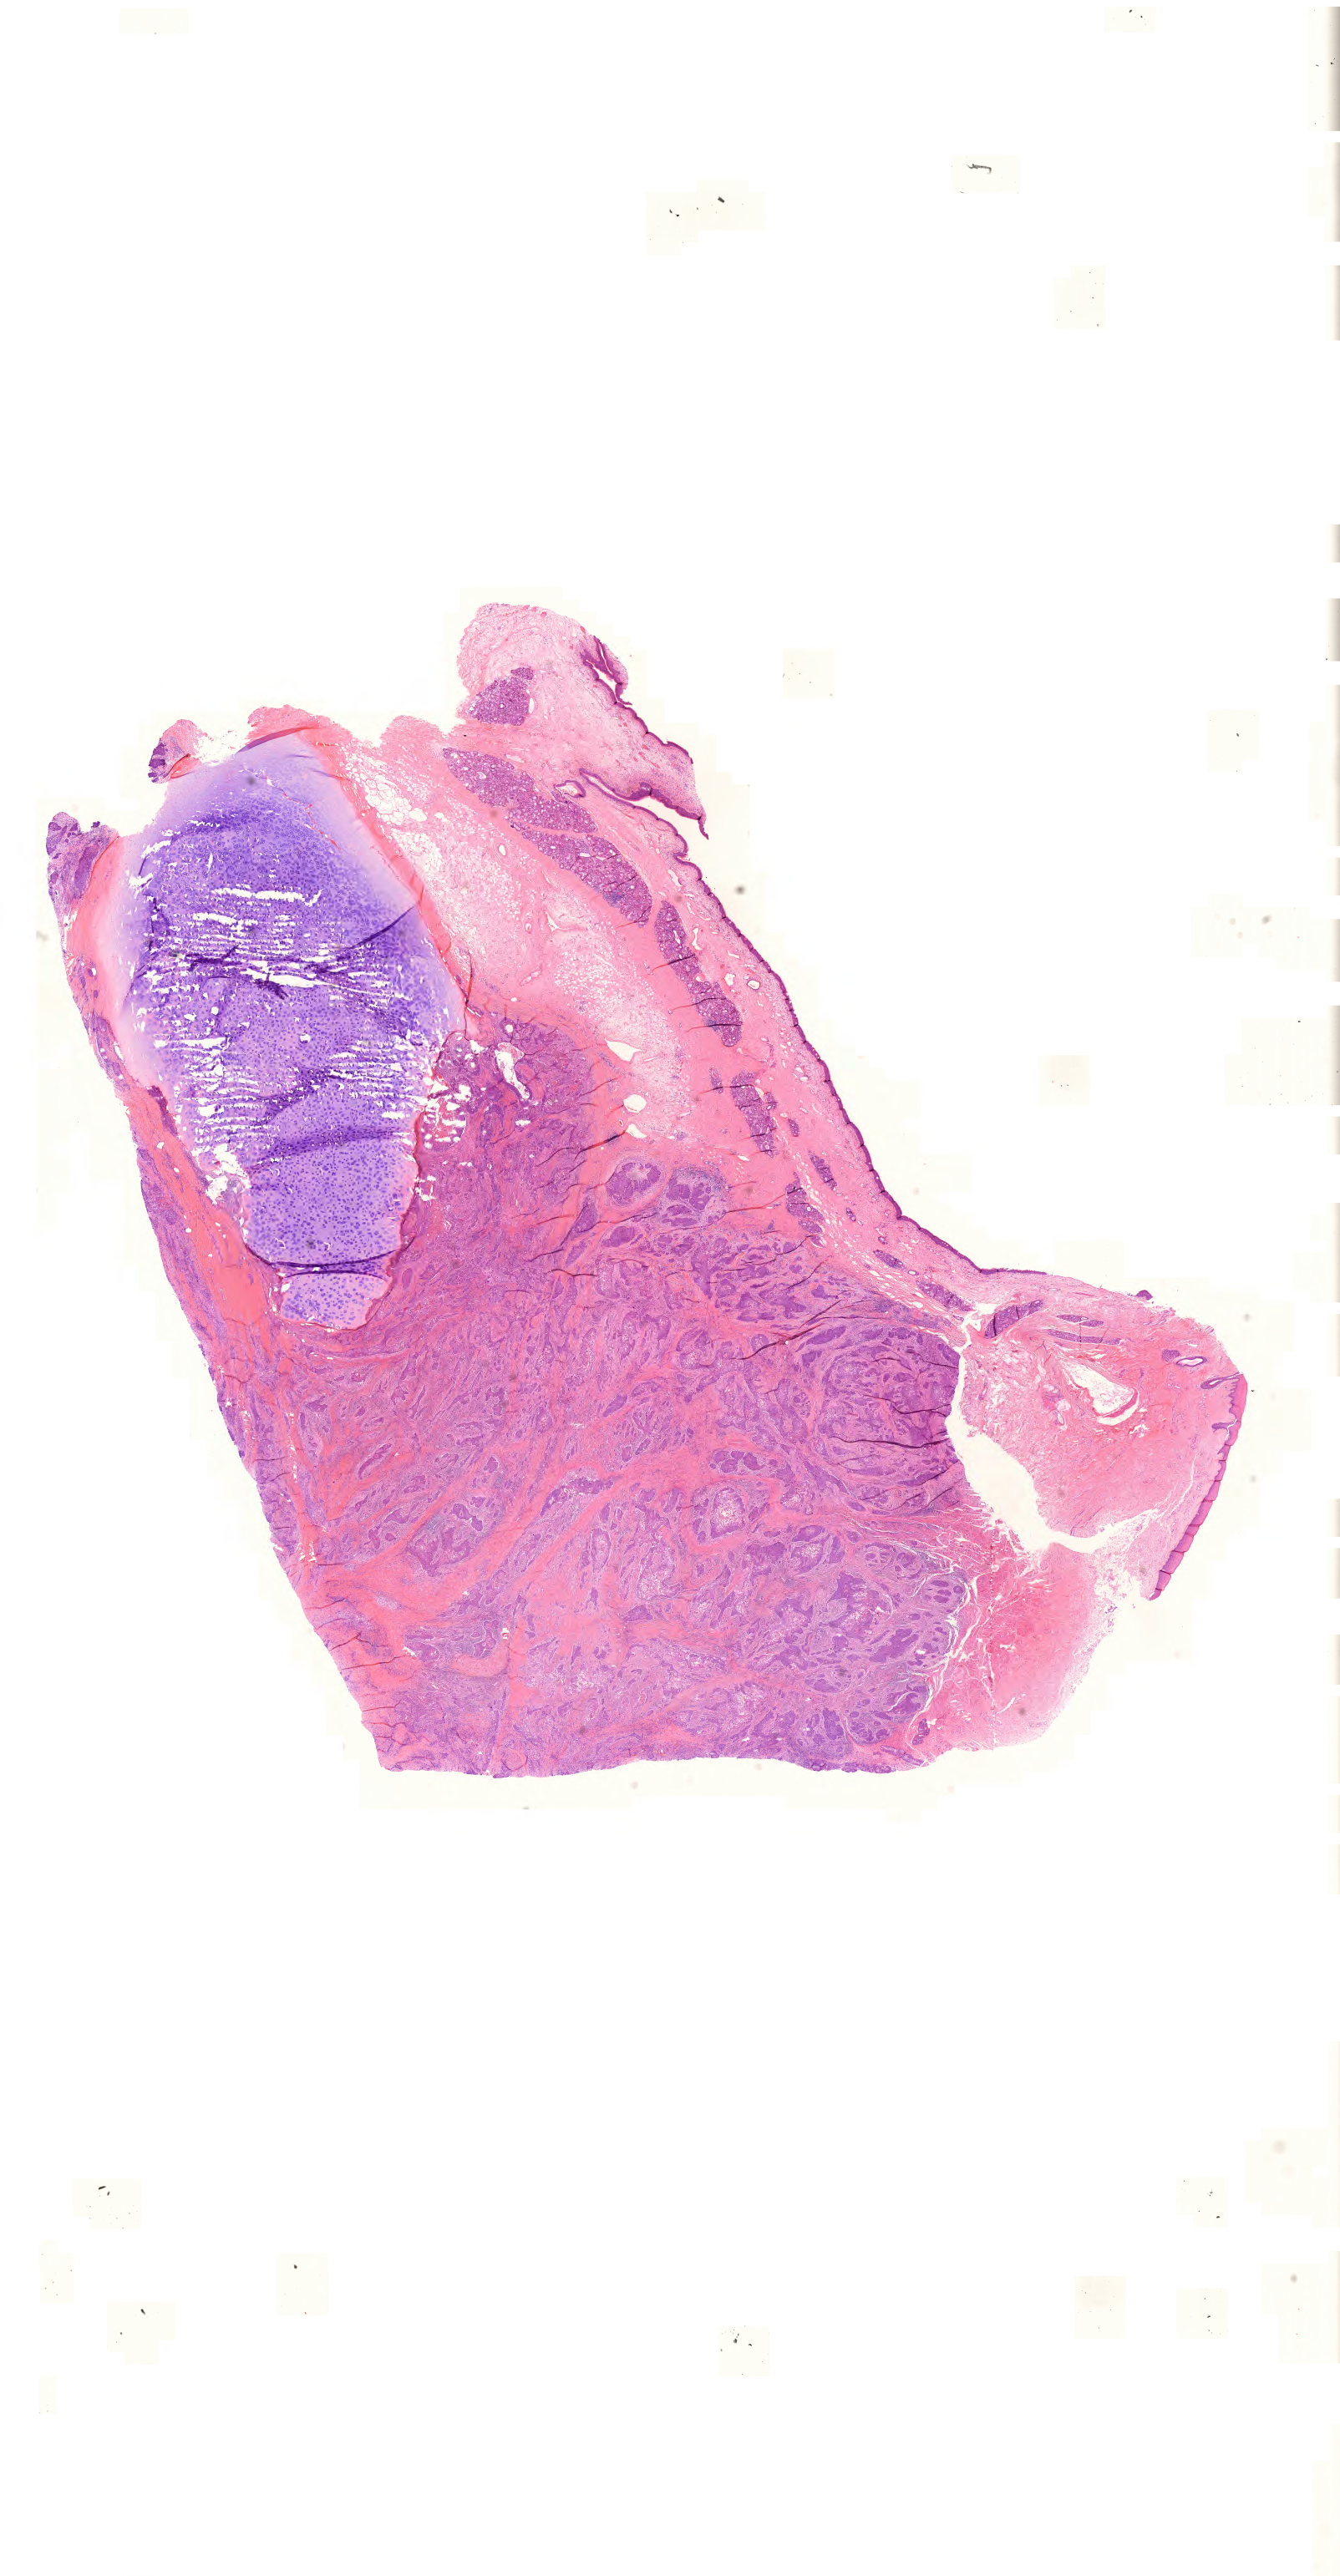
Whole-slide histology image, H&E — low-resolution overview of the scanned area, about 23.9 x 45.9 mm; formalin-fixed paraffin-embedded (FFPE) diagnostic section; sample: primary tumour, head and neck. Patient: male, age at initial diagnosis 52 years. Histologic grade: G2 (moderately differentiated).
- AJCC pathologic stage: IVA (7th edition)
- histologic diagnosis: Squamous cell carcinoma, NOS (larynx, NOS)
- laterality: midline